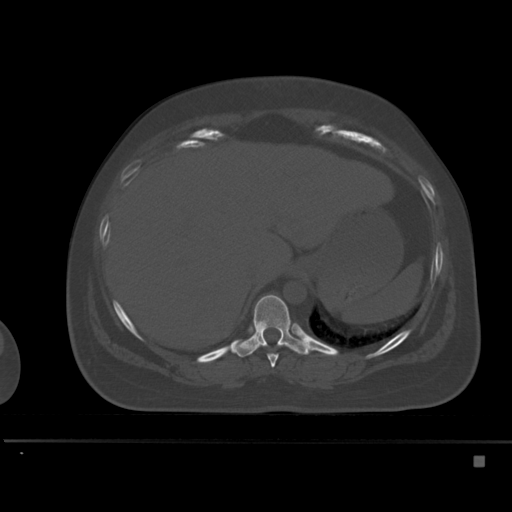
CT including the spine, one axial slice. Slice 252 of 495 in the series (ordered by position). Bone window (W 1800 / L 400 HU). 512 × 512 image matrix, field of view 404 × 404 mm. Female patient, age 33 years. From the clinical record (not read from this slice): primary cancer: breast.
Annotated regions visible in this slice (semi-automatic segmentation, software-assisted and operator-edited):
- T10 vertebra: box from (x=234, y=295) to (x=310, y=357) px
- T9 vertebra: (x=267, y=353)–(x=279, y=368)